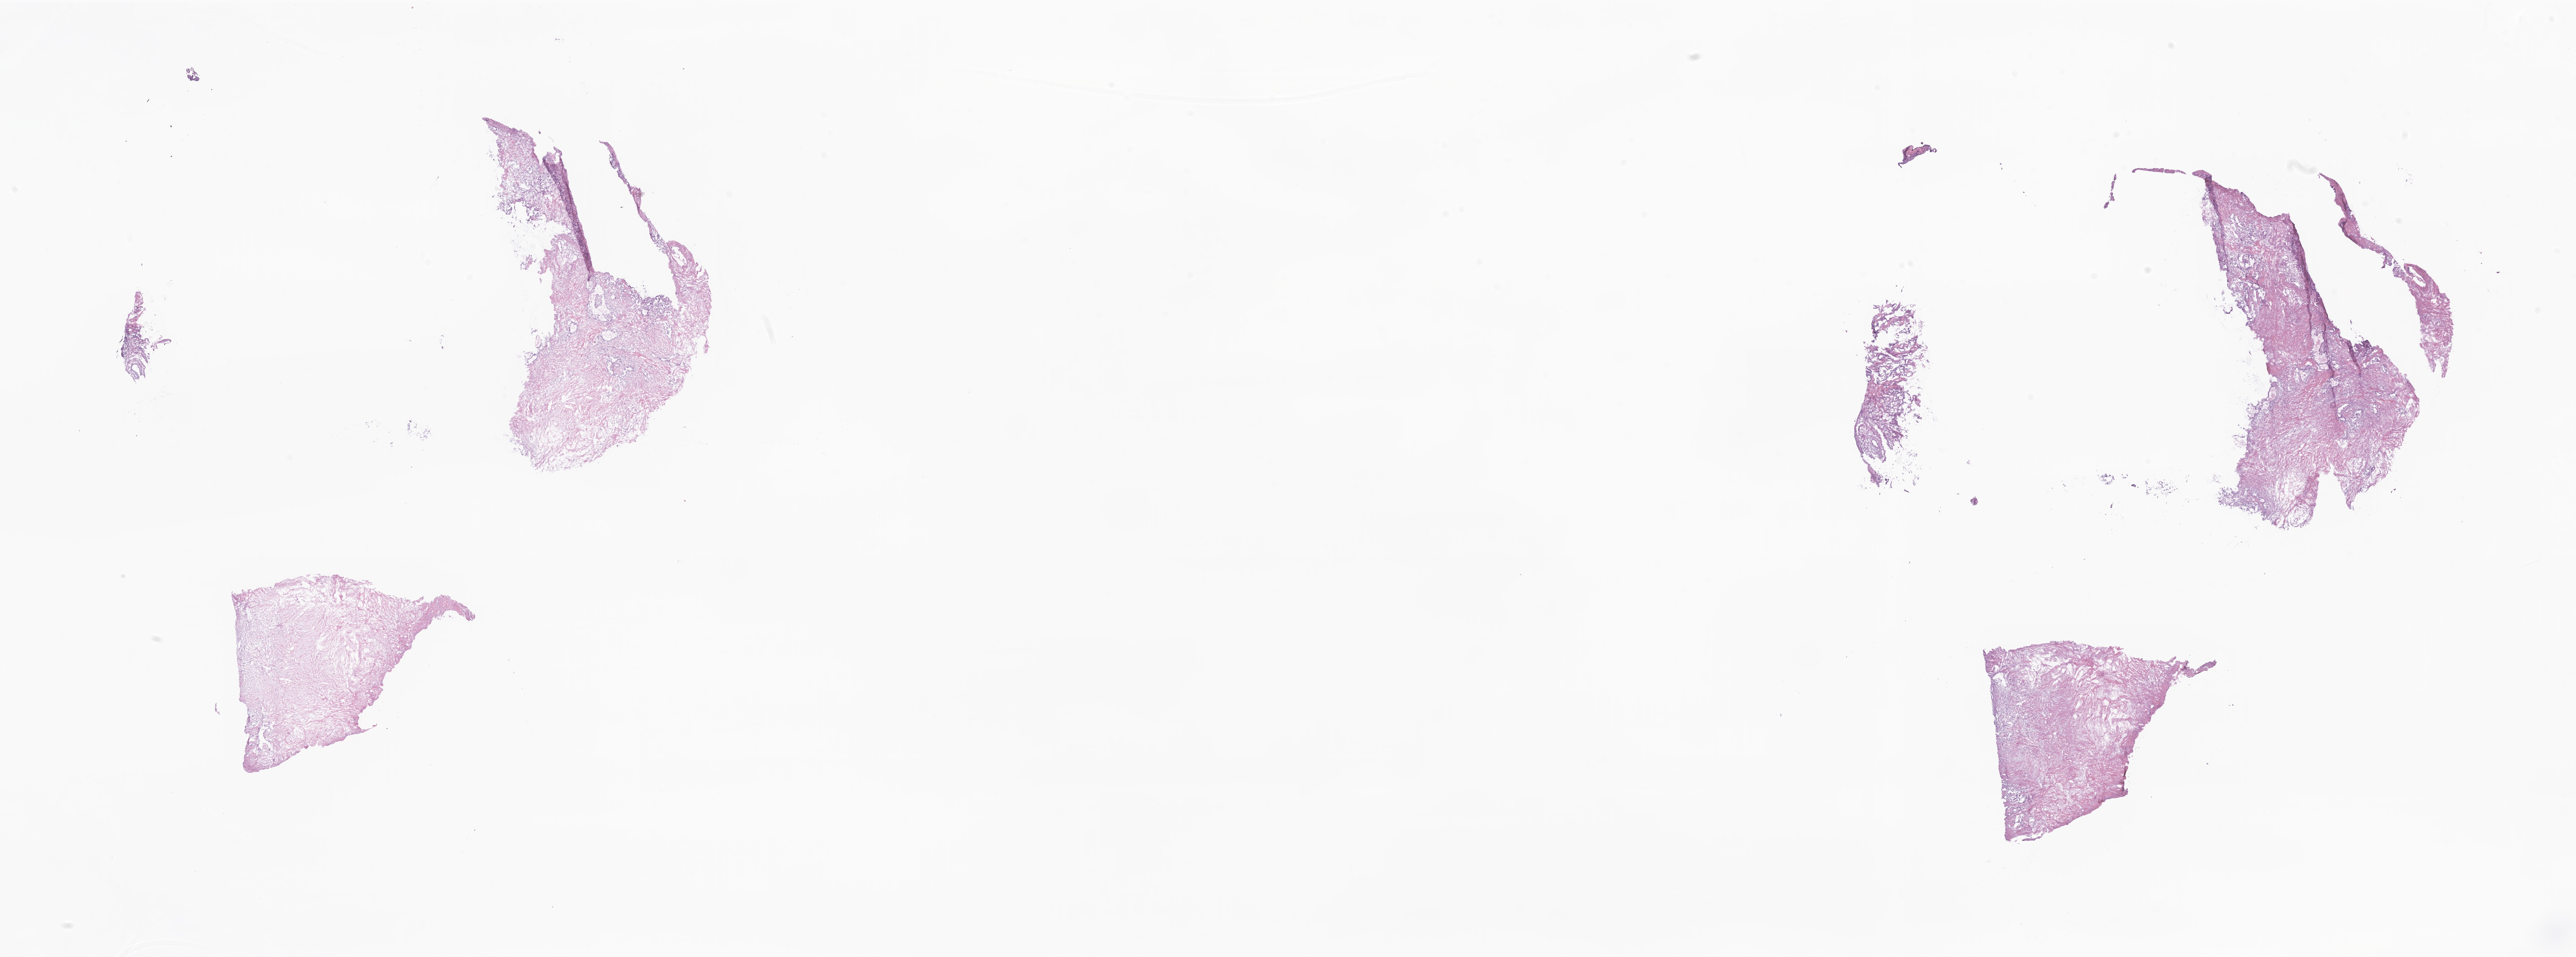
Digitized H&E-stained section — a low-resolution overview of the entire scanned area, about 40.9 x 15.2 mm, frozen section, specimen: primary tumor, site: head of pancreas. Patient: male, age at initial diagnosis 77 years. Tumor grade: G2 (moderately differentiated). Composition of this section per pathologist review: tumor cells 65%, tumor nuclei 65%, stromal cells 35%, necrosis 0%, normal cells 0%. Infiltration values recorded for this section: lymphocyte infiltration 7%, monocyte infiltration 2%, neutrophil infiltration 8%.
AJCC pathologic stage: Stage IB. Diagnosis: Intraductal papillary mucinous neoplasm with invasive carcinoma.